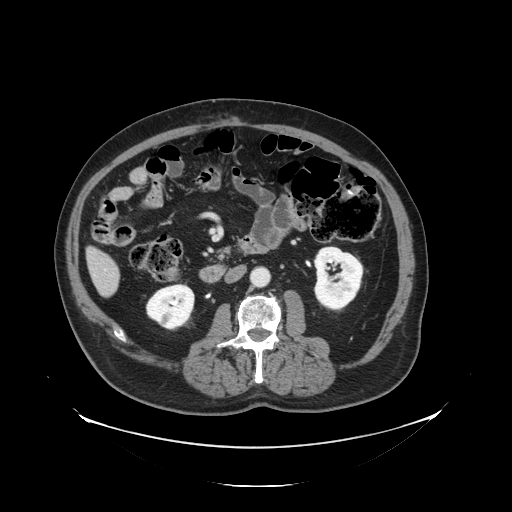
Contrast-enhanced abdominal CT, one axial slice; position 38 of 138 along the scan axis; reconstruction kernel STANDARD; 120 kVp; intravenous contrast given; soft-tissue window (W 400 / L 40 HU); 2.5 mm slice thickness; 512 × 512 image matrix, field of view 497 × 497 mm. Male patient, age 77 years. From the clinical record (not read from this slice): diagnosis: colorectal cancer liver metastases, imaged before liver resection; multiple liver metastases: no; largest metastasis: 1.5 cm; disease in both lobes: no.
Structures marked on this image (expert manual segmentation):
- liver: bounding box (x1, y1, x2, y2) in pixels: (89, 250, 120, 296)
- planned liver remnant (the part of the liver to remain after resection): (89, 250, 116, 275)